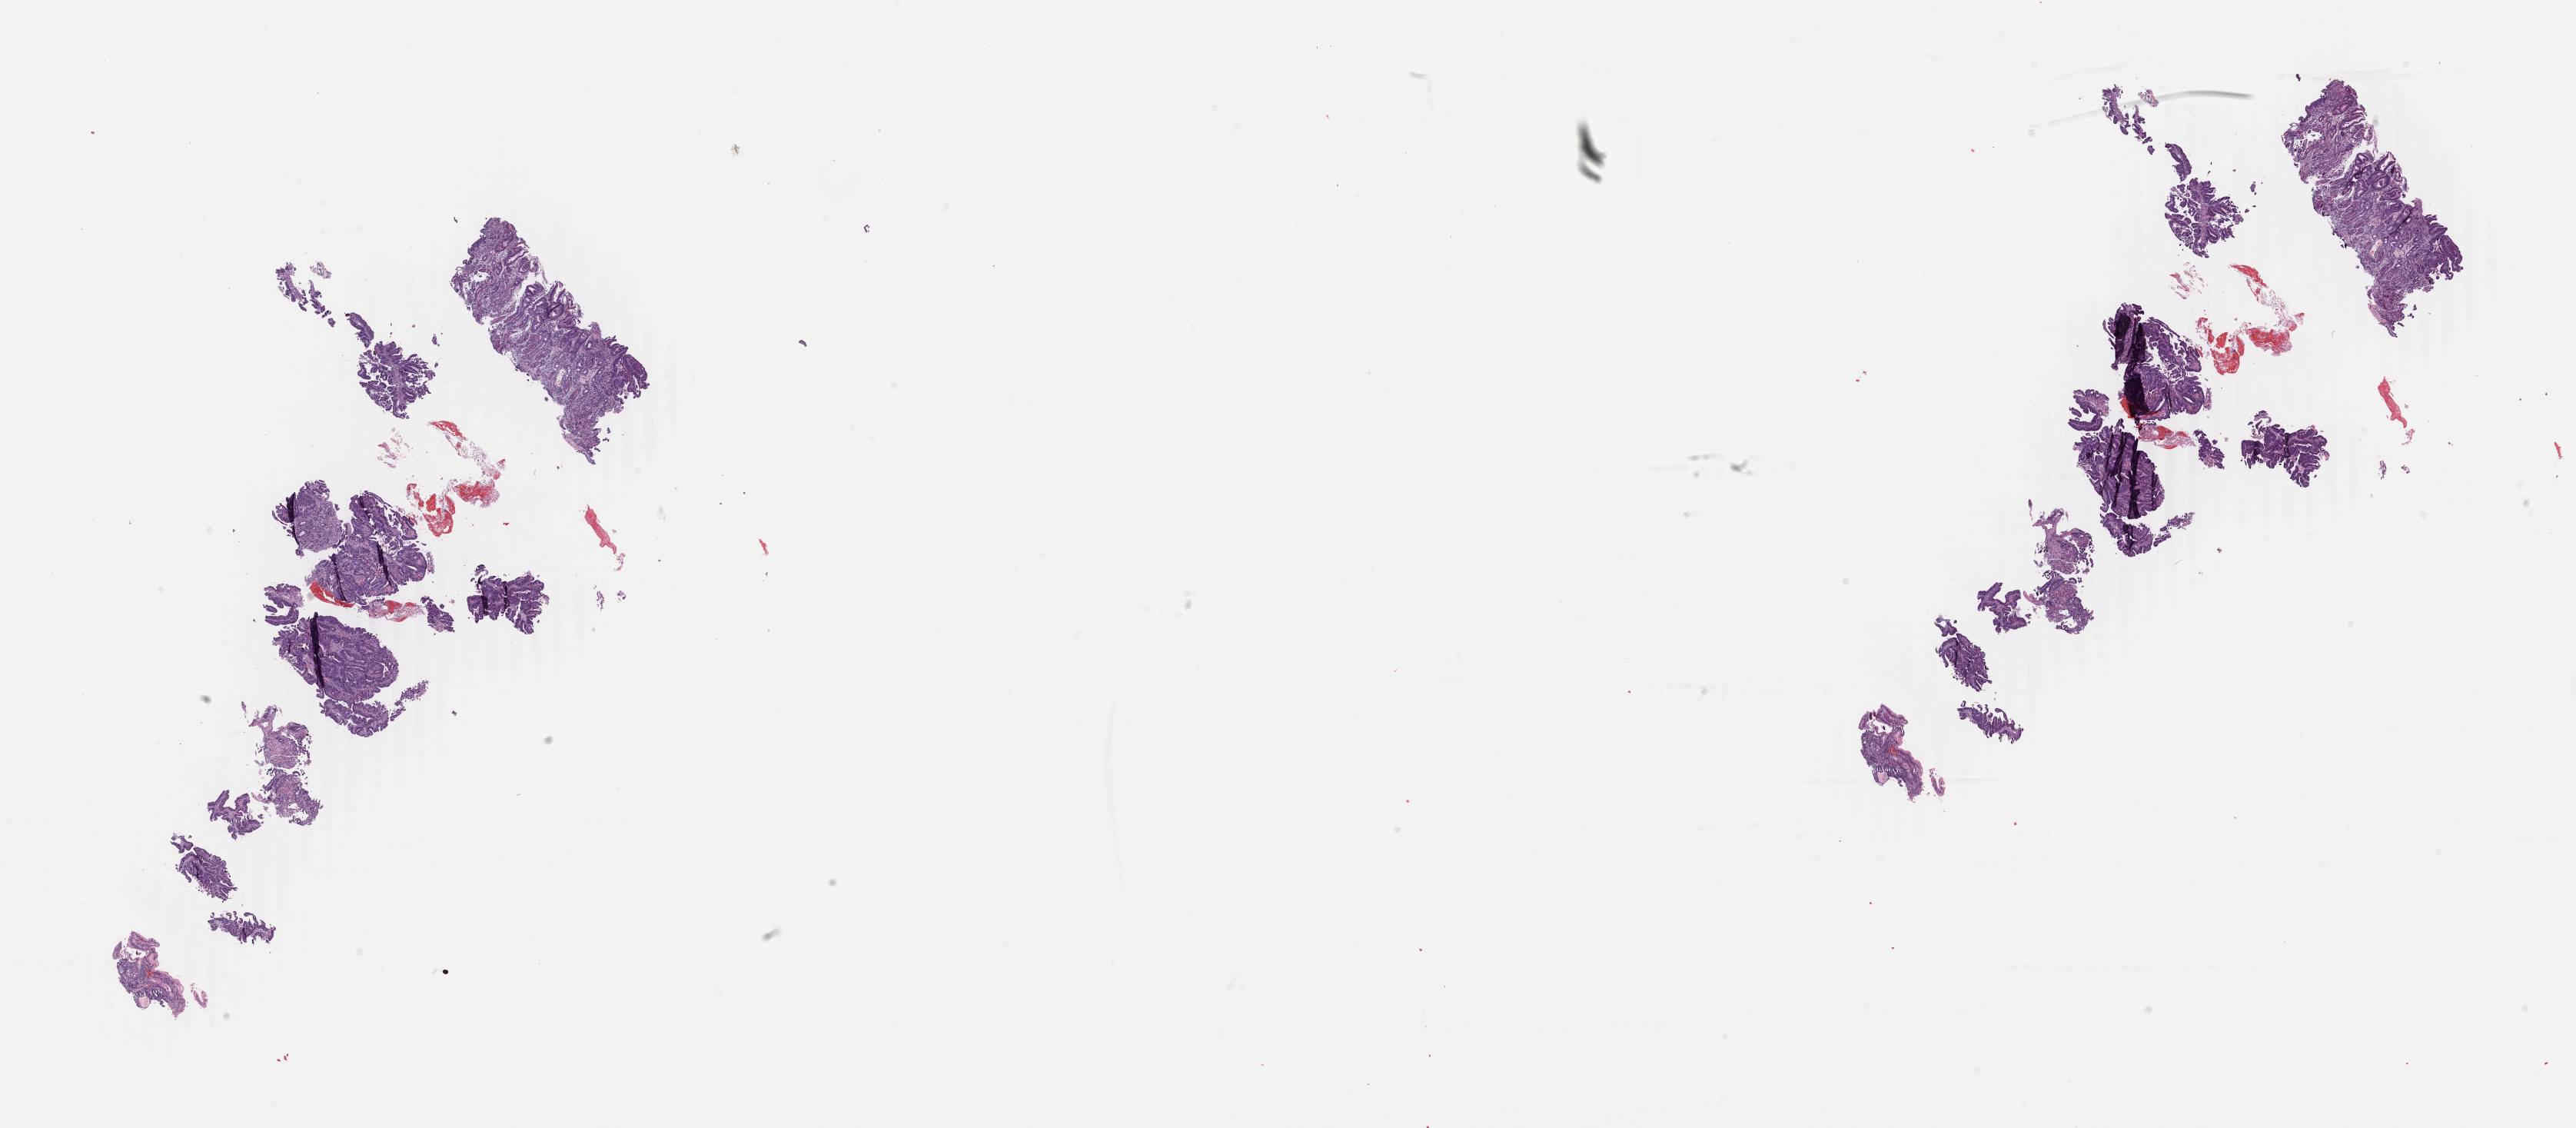
Whole-slide histology image, H&E-stained — a low-resolution overview of the entire scanned area, about 26.7 x 11.7 mm, formalin-fixed paraffin-embedded (FFPE) diagnostic section, stomach, primary tumour sample. Female patient; age at initial diagnosis 66 years. Histologic grade: G2 (moderately differentiated). Pathologist review of this section (percent, as recorded): tumour cells 55%, tumour nuclei 75%, normal cells 15%, stromal cells 25%, necrosis 5%. Infiltration values recorded for this section: lymphocyte infiltration 10%, monocyte infiltration 2%, neutrophil infiltration 2%.
* histologic diagnosis: Tubular adenocarcinoma (cardia, NOS)
* AJCC pathologic stage: IIIA (7th edition)